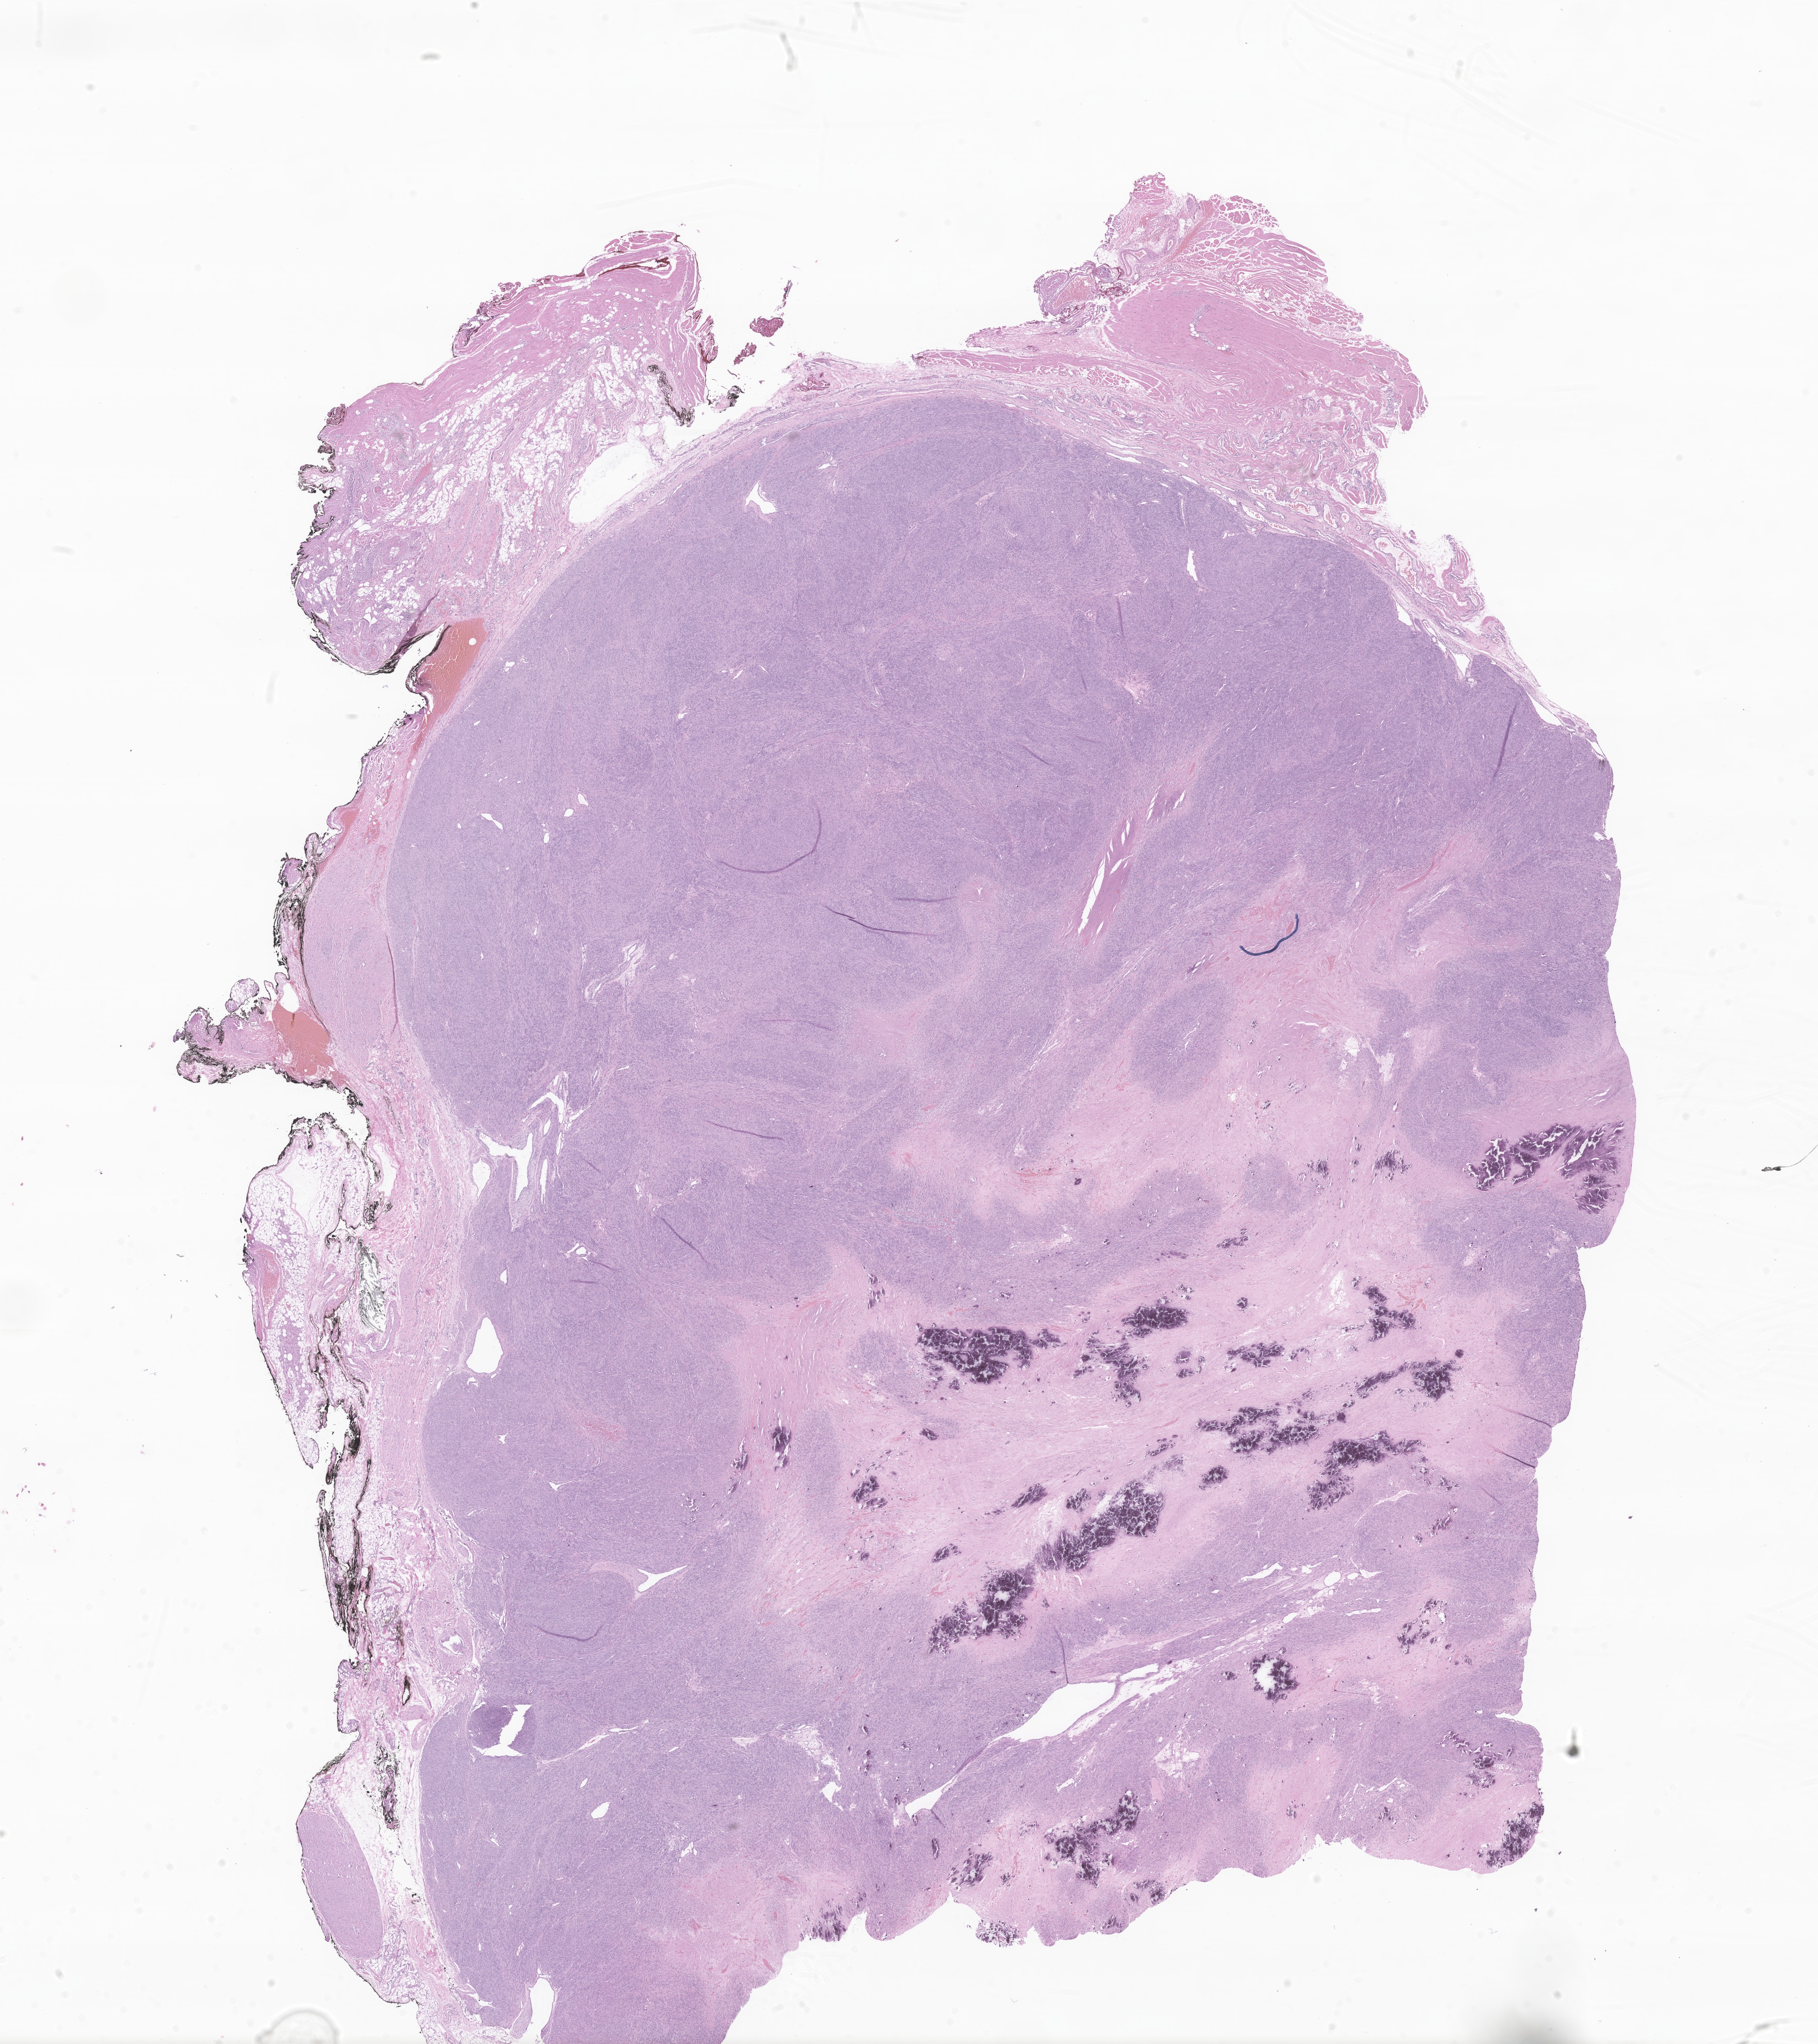
Digitized haematoxylin and eosin-stained section of tumor tissue from the thorax, a low-resolution overview of the entire scanned area, about 18.9 x 21.3 mm; formalin-fixed, paraffin-embedded (FFPE) tissue. Female patient, age 89 months.
- recorded diagnosis: Leiomyosarcoma, NOS